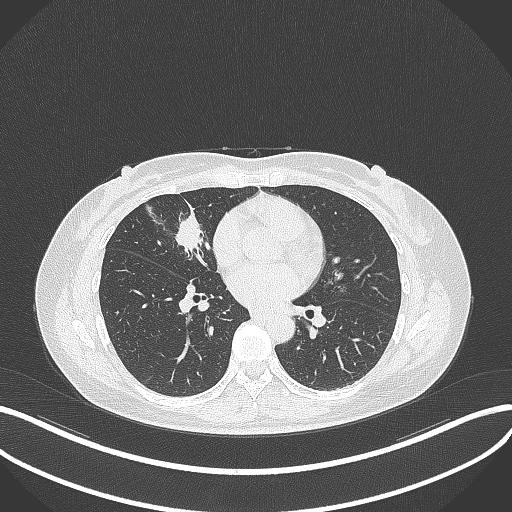
Chest CT, one axial slice. Position 138 of 284 along the scan axis. Reconstruction kernel B70f. Lung window (W 1500 / L -600 HU). 1 mm slice thickness. 512 × 512 image matrix, field of view 400 × 400 mm. Patient: female, 43 years. Case-level facts recorded for this patient, not image findings: clinical TNM (as recorded): T1c N3 M1.
Outlined on this slice (bounding box drawn by a radiologist):
- lung tumour (recorded histology: adenocarcinoma): bounding box <175,209,208,261> (left, top, right, bottom; pixels)